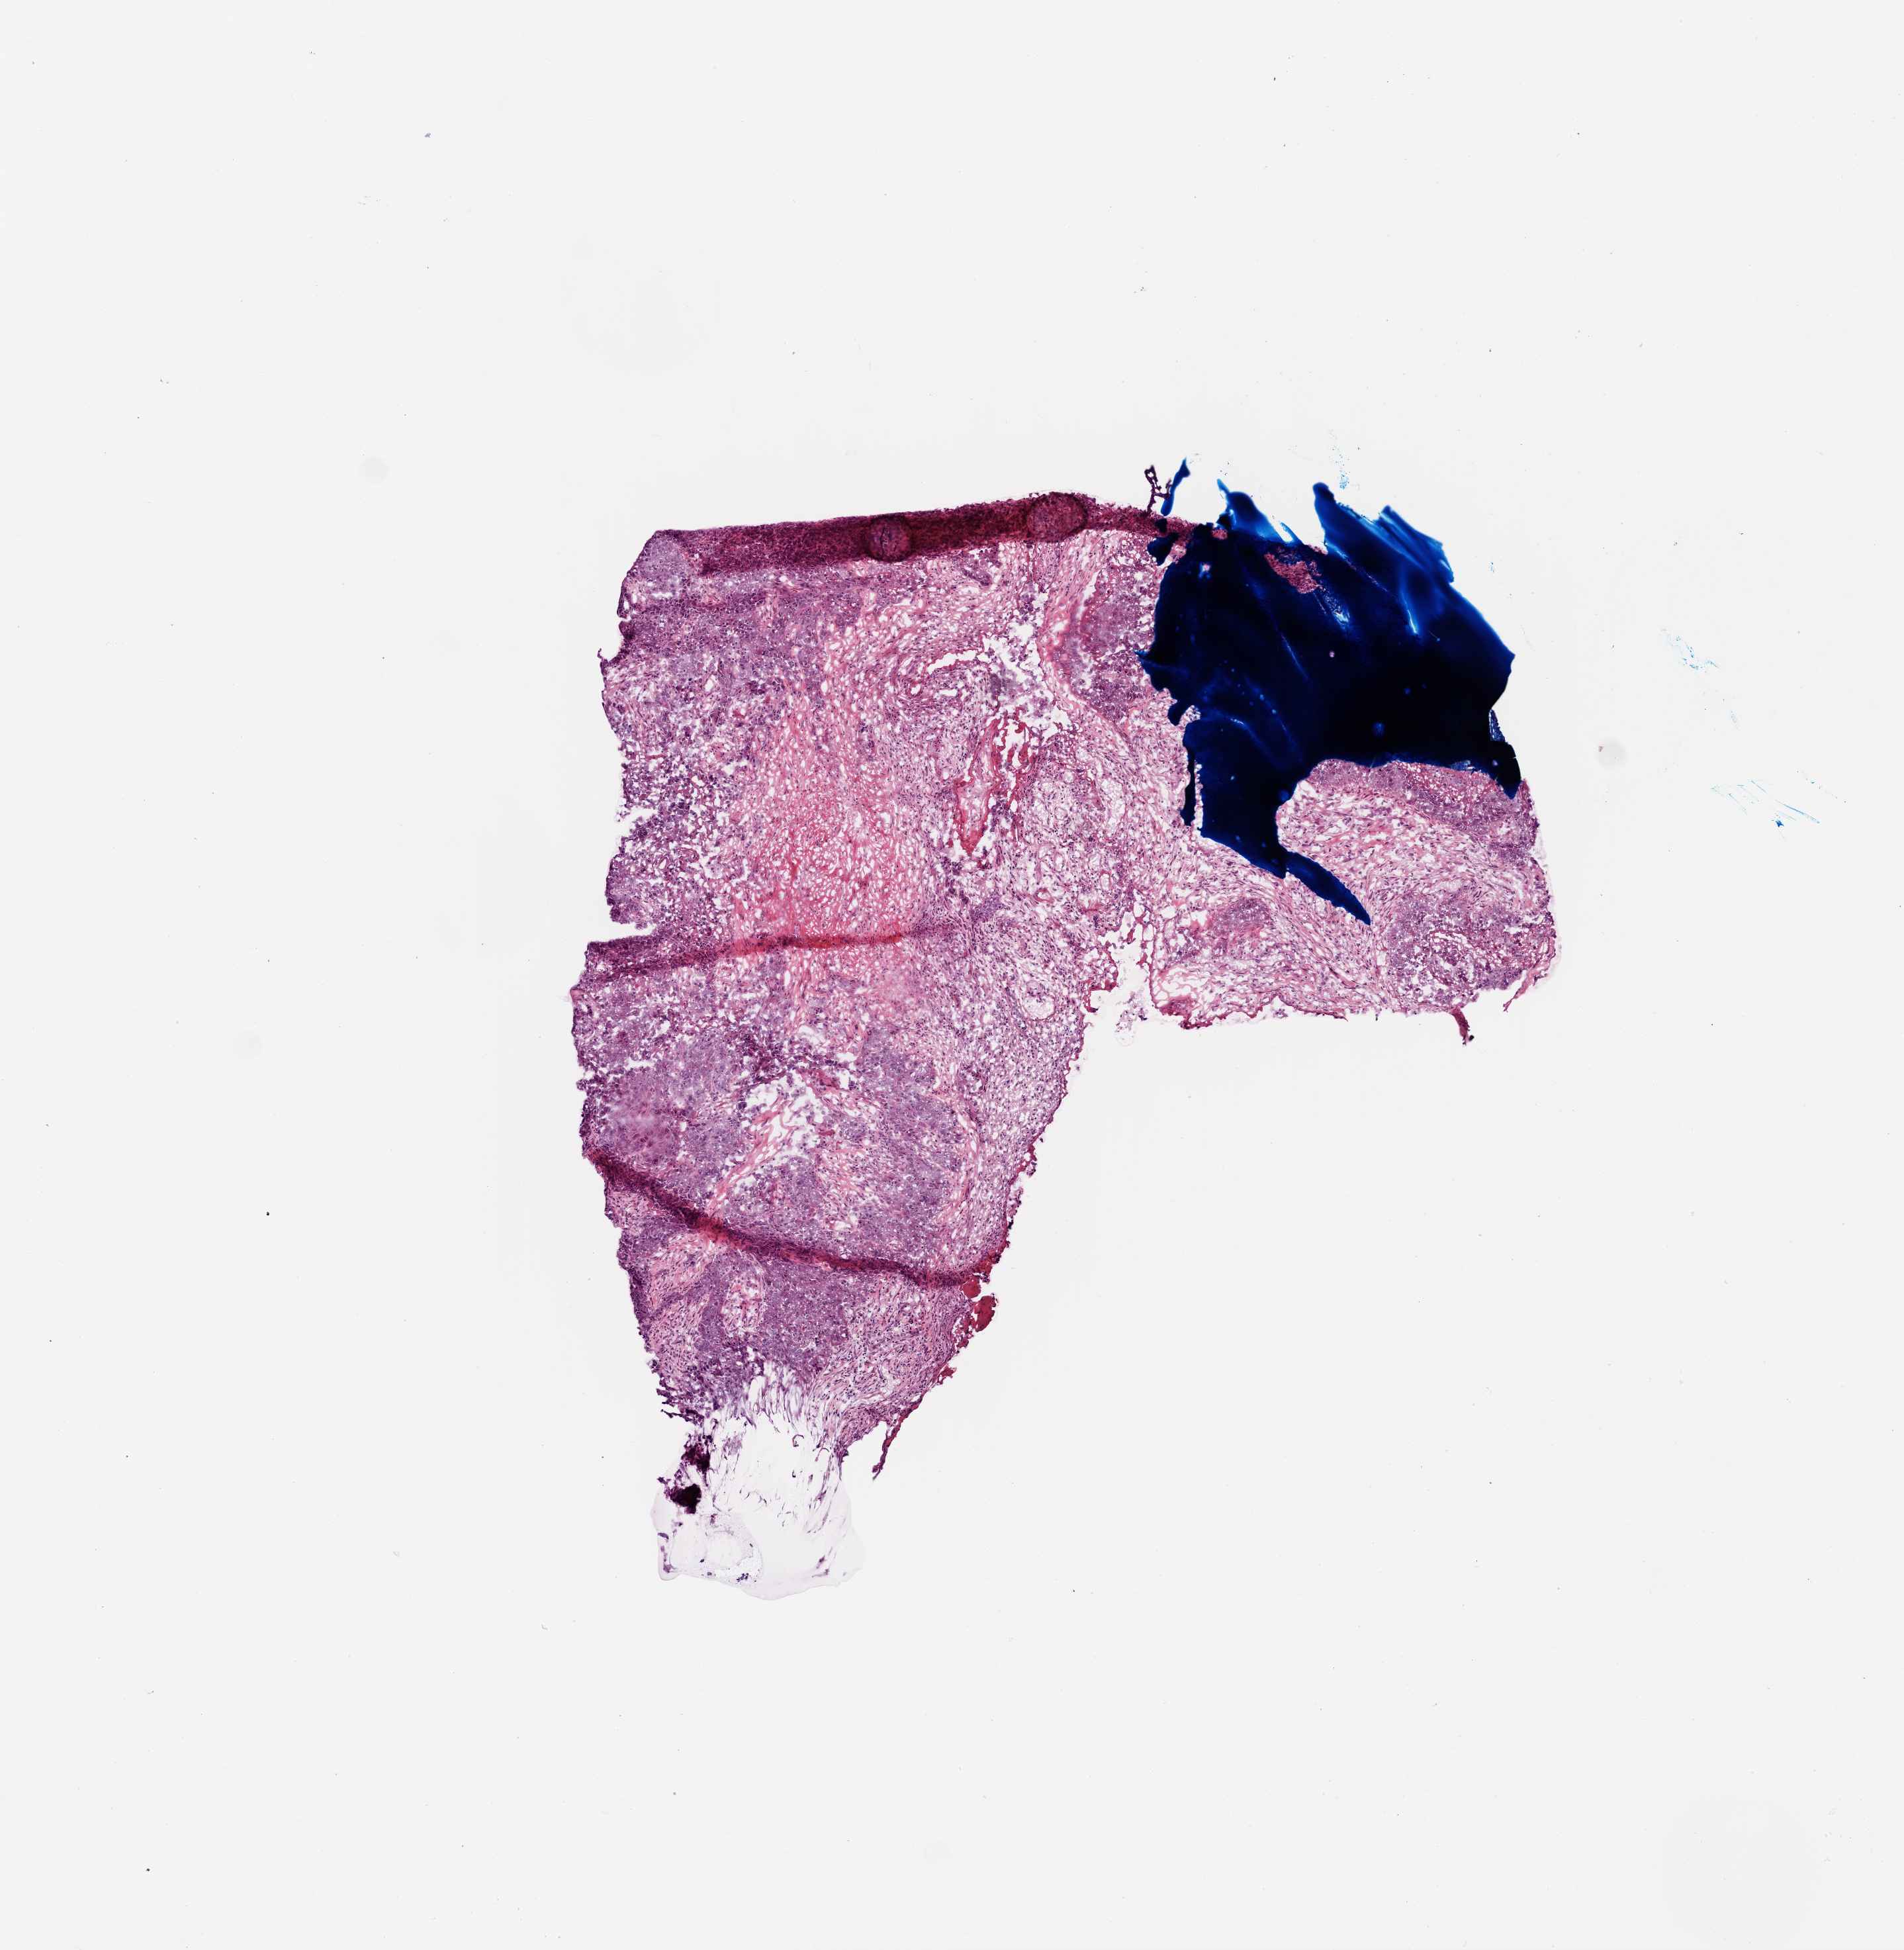
Whole-slide histology image, H&E, low-resolution overview of the scanned area, about 5.8 x 5.9 mm (from a 20x scan), frozen section from the top of the tissue portion, primary tumour sample from the ovary. Female patient; age at initial diagnosis 70 years. Histologic grade: G3 (poorly differentiated). Slide review estimates, as recorded: tumour cells 70%, tumour nuclei 80%, normal cells 10%, stromal cells 20%, necrosis 0%.
Diagnosis: Serous cystadenocarcinoma, NOS. Laterality: left. FIGO stage: IIIC.